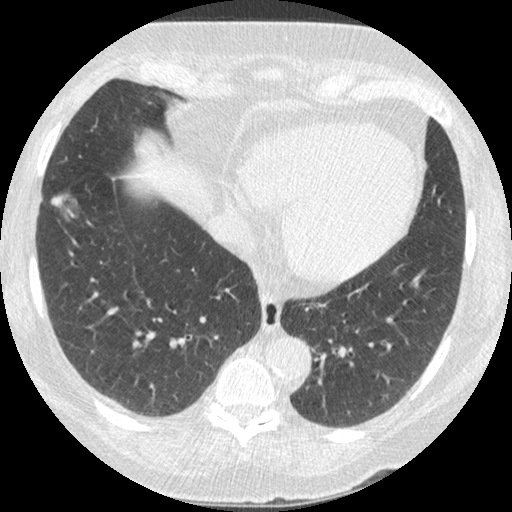
Low-dose screening chest CT, one axial slice; slice 91 of 245 in the series (ordered by position); 120 kVp; lung window (W 1500 / L -600 HU); 512 × 512 image matrix, field of view 310 × 310 mm.
Outlined on this slice (outlined manually by an expert reader):
- lesion 1 (tumor, lower lobe of right lung): box from (x=51, y=194) to (x=78, y=220) px